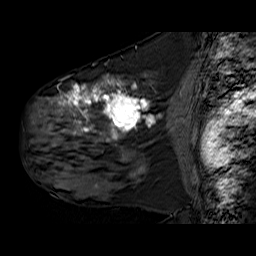
Breast MRI (dynamic contrast-enhanced), one sagittal slice; slice 35 of 60 in the series (ordered by position); dynamic contrast-enhanced series, time point 2 of 6 at this slice position (early post-contrast); 1.5 T; TE 6.3 ms, TR 32.9 ms; 4 mm slice thickness; 256 × 256 image matrix, field of view 200 × 200 mm. Female patient. From the clinical record (not read from this slice): setting: breast cancer imaged before/during neoadjuvant chemotherapy; receptor status: HER2-positive.
Outlined on this slice (semi-automatically segmented with operator editing):
- analysis volume of interest (the breast-tissue region the enhancement analysis was run in; not a lesion): bounding box <30,78,174,180> (left, top, right, bottom; pixels)
- tumour enhancement mask (voxels above the 100 % enhancement threshold inside the analysis volume of interest): <59,79,150,176>